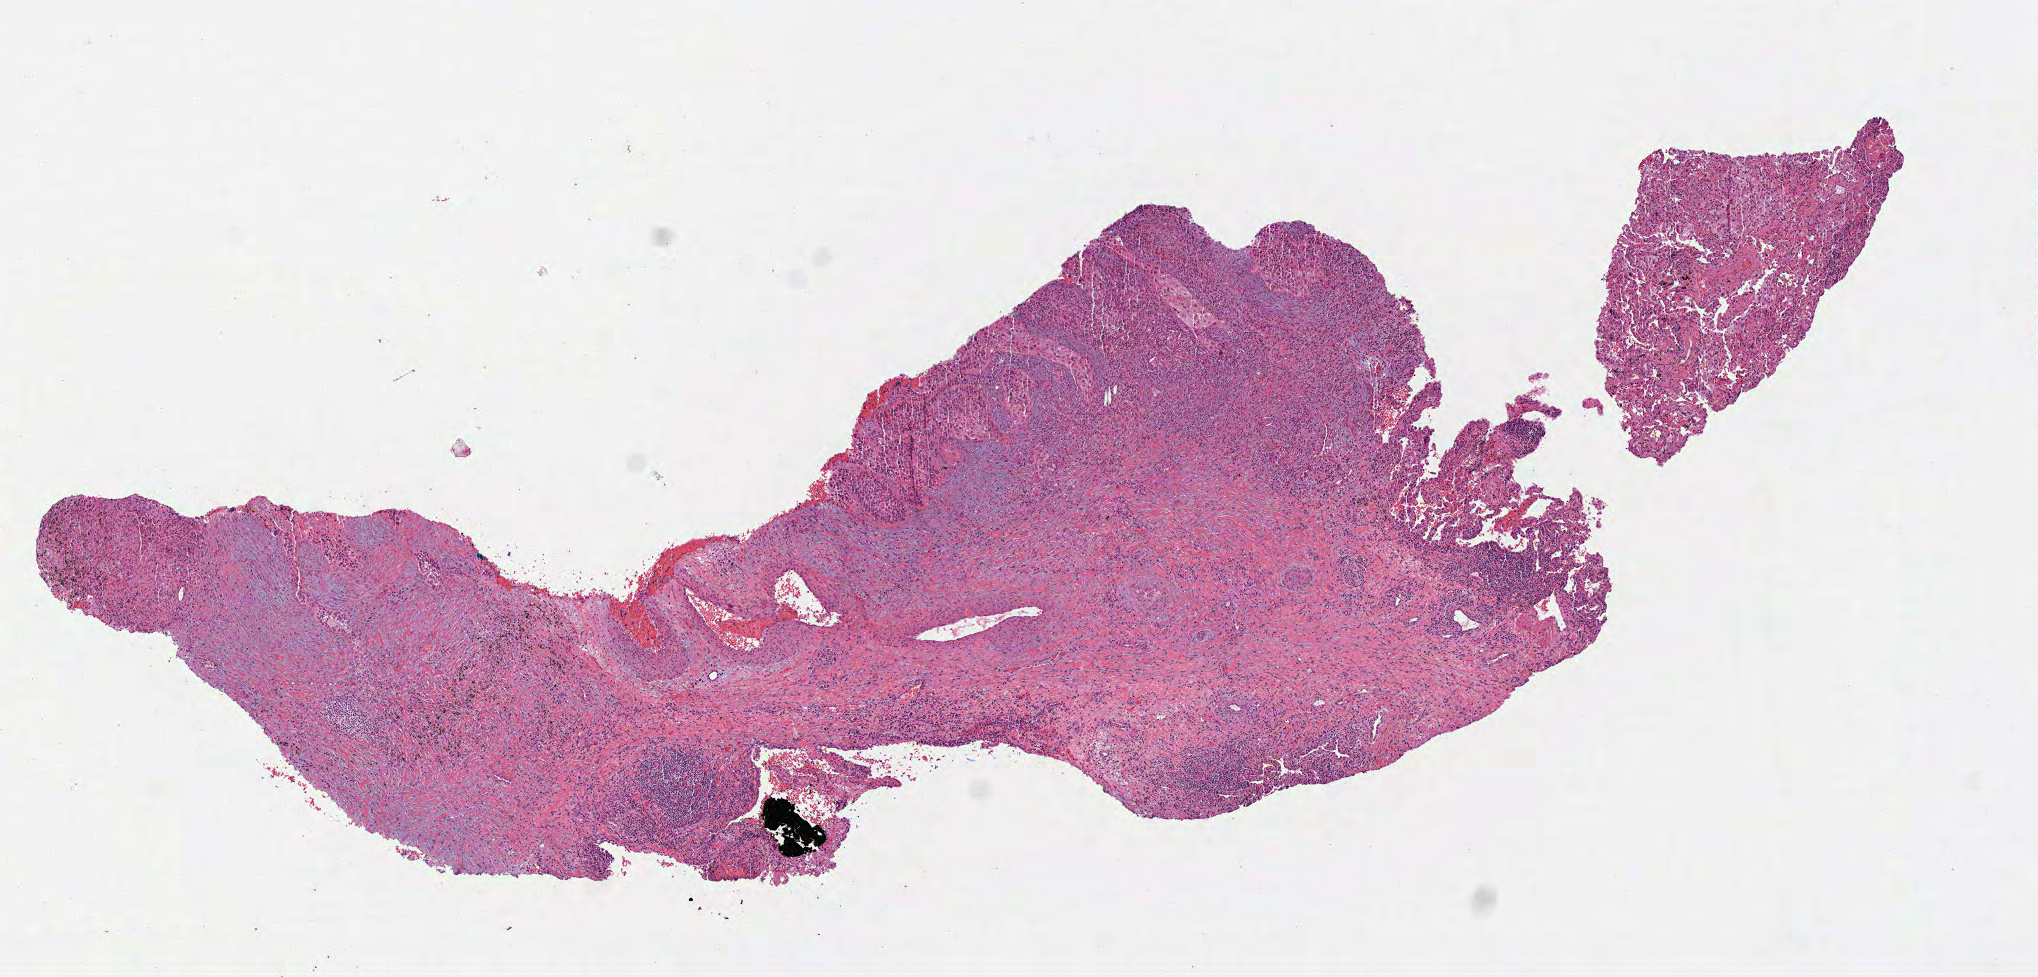
Digitized H&E tissue section (whole slide), low-resolution overview of the scanned area, about 8.2 x 3.9 mm, formalin-fixed paraffin-embedded (FFPE) diagnostic section, lung, primary tumour sample. Patient: male, age at initial diagnosis 78 years.
AJCC pathologic stage: IA (7th edition). Diagnosis: Squamous cell carcinoma, NOS (upper lobe, lung). TNM: T1b N0 MX.